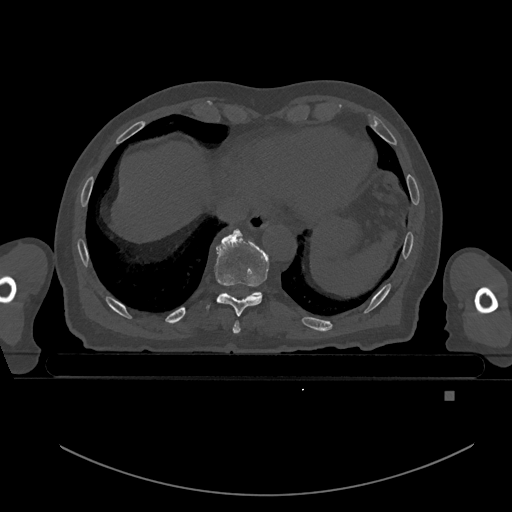
CT including the spine, one axial slice. Position 138 of 969 along the scan axis. Bone window (W 1800 / L 400 HU). 512 × 512 image matrix, field of view 456 × 456 mm. Patient: male, 82 years. From the clinical record (not read from this slice): primary cancer: prostate.
Outlined on this slice (semi-automatically segmented with operator editing):
- T10 vertebra: box from (x=254, y=292) to (x=261, y=295) px
- T8 vertebra: (x=232, y=321)–(x=240, y=334)
- T9 vertebra: (x=206, y=230)–(x=269, y=316)